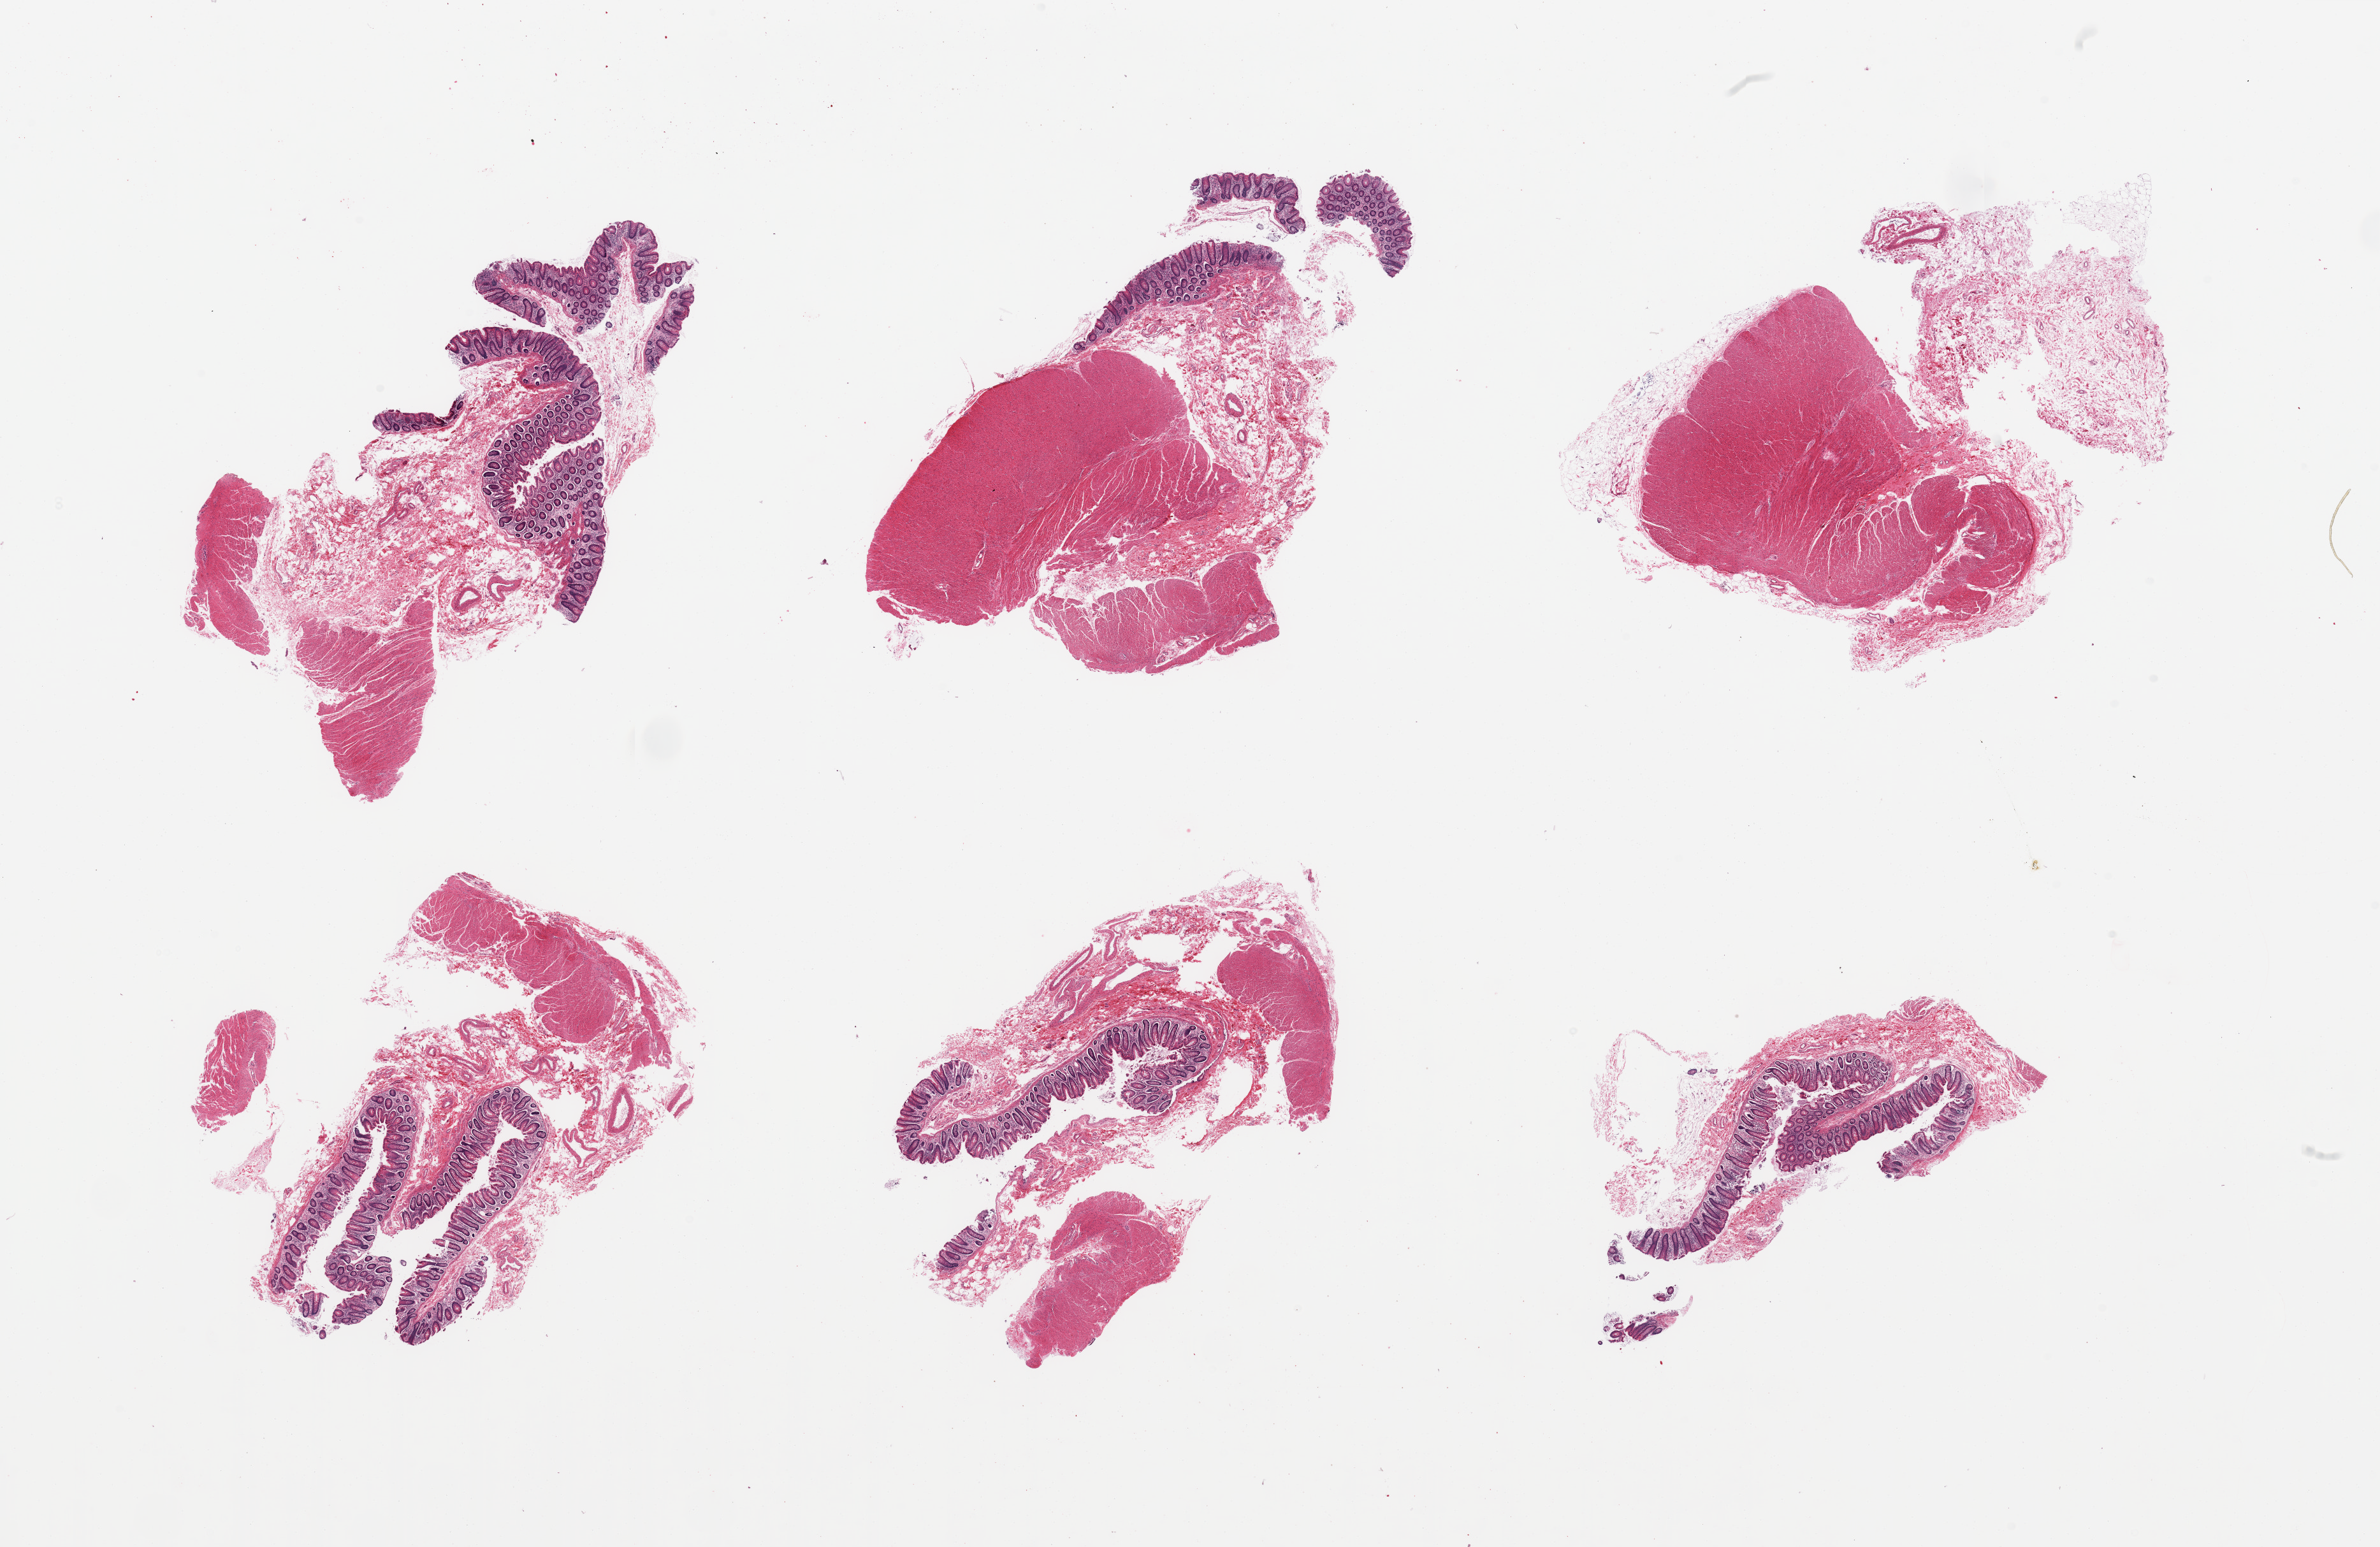
Digitized H&E-stained section, brightfield — a low-resolution overview of the entire scanned area, about 29.5 x 19.2 mm; PAXgene-fixed paraffin-embedded (PFPE) section; sampled site (target tissue): ileum; donor tissue sample. Donor sex: male.
* reviewer comment on this tissue sample: 6 pieces; colon sampled, not ileum